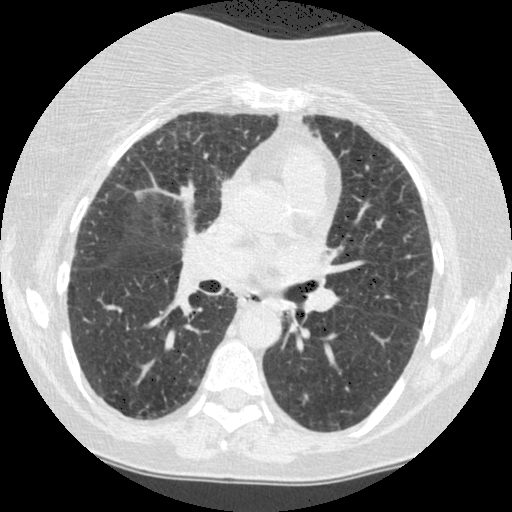
Axial slice from a low-dose chest CT screening exam, baseline screening round, lung window (W 1500 / L -600 HU), standard (soft-tissue) reconstruction kernel (STANDARD), 512 × 512 image matrix. Female participant, aged 60 years at enrolment. Former smoker at enrolment.
Expert reader's lesion annotation, bounding box <269,293,310,335> (left, top, right, bottom; pixels). The screening reader recorded 2 non-calcified nodules or masses ≥4 mm on this exam (right lower lobe, left lower lobe); which of them this box marks is not recorded. Official screen result: positive, change unspecified: nodule(s) >= 4 mm or enlarging nodule(s), mass(es), or other non-specific abnormalities suspicious for lung cancer.